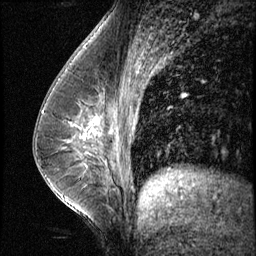
Breast MRI (dynamic contrast-enhanced), one sagittal slice. Slice 33 of 60 in the series (ordered by position). 3 images stored at this slice position (order not interpretable as contrast timing). 1.5 T. TE 4.2 ms, TR 8.7 ms. 256 × 256 image matrix, field of view 180 × 180 mm. Patient: female, 35 years. Case-level facts recorded for this patient, not image findings: setting: breast cancer imaged before/during neoadjuvant chemotherapy; receptor status: HER2-positive.
Annotated regions visible in this slice (semi-automatic segmentation, software-assisted and operator-edited):
- analysis volume of interest (the breast-tissue region the enhancement analysis was run in; not a lesion): box from (x=65, y=102) to (x=121, y=156) px
- tumour enhancement mask (voxels above the 140 % enhancement threshold inside the analysis volume of interest): (x=94, y=118)–(x=98, y=131)